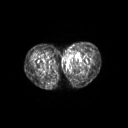
FDG PET of an extremity soft-tissue mass (from a PET/CT study), one axial slice. Slice 42 of 267 in the series (ordered by position). 3.27 mm slice thickness. 128 × 128 image matrix, field of view 600 × 600 mm. Patient: female, 24 years. Case-level facts recorded for this patient, not image findings: histological type: leiomyosarcoma; grade: high; site of the primary tumour: groin.
Structures marked on this image (expert contour drawn on MRI and transferred to this co-registered scan by the dataset authors):
- gross tumour volume including surrounding oedema: bounding box [x1, y1, x2, y2] px = [61, 49, 79, 64]